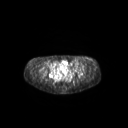
FDG PET of an extremity soft-tissue mass (from a PET/CT study), one axial slice; position 79 of 267 along the scan axis; 3.27 mm slice thickness; 128 × 128 image matrix. Female patient, age 24 years. From the clinical record (not read from this slice): histological type: leiomyosarcoma; grade: high; site of the primary tumour: groin.
Outlined on this slice (expert contour drawn on MRI and transferred to this co-registered scan by the dataset authors):
- gross tumour volume including surrounding oedema: bounding box (x1, y1, x2, y2) in pixels: (77, 59, 93, 64)
- gross tumour volume (mass): (79, 61, 82, 63)